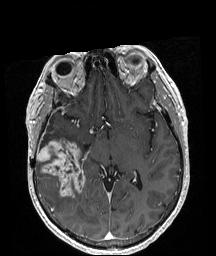
Brain MRI from a brain-tumour surgery series, one axial slice. Slice 111 of 208 in the series (ordered by position). T1-weighted post-contrast. 1 mm slice thickness. 216 × 256 image matrix, field of view 211 × 250 mm. Case-level facts recorded for this patient, not image findings: histopathology: Astrocytoma; WHO grade: 4.
Outlined on this slice (outlined manually by an expert reader):
- tumour: bounding box (x1, y1, x2, y2) in pixels: (37, 140, 84, 198)